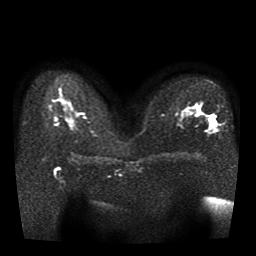
Breast MRI, one axial slice; position 21 of 41 along the scan axis; diffusion-weighted series; image 2 of 4 stored at this slice position (different b-values; order by instance number); 1.5 T; 5 mm slice thickness; 256 × 256 image matrix, field of view 330 × 330 mm. Female patient.
Structures marked on this image (expert manual segmentation):
- tumour on diffusion-weighted imaging: bounding box <209,119,214,126> (left, top, right, bottom; pixels)